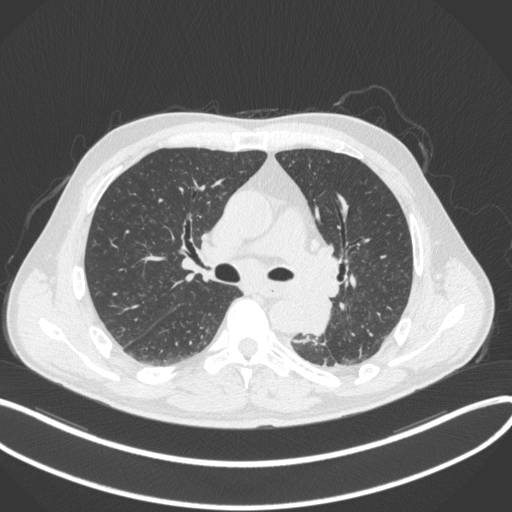
Chest CT, one axial slice; position 208 of 328 along the scan axis; reconstruction kernel B31f; 120 kVp; lung window (W 1500 / L -600 HU); 1 mm slice thickness; 512 × 512 image matrix, field of view 400 × 400 mm. Patient: male, 59 years. Case-level facts recorded for this patient, not image findings: clinical TNM (as recorded): T2a N2 M0.
Annotated regions visible in this slice (rectangle marked by the reading radiologist):
- lung tumour (recorded histology: squamous cell carcinoma): bounding box (x1, y1, x2, y2) in pixels: (303, 289, 334, 338)